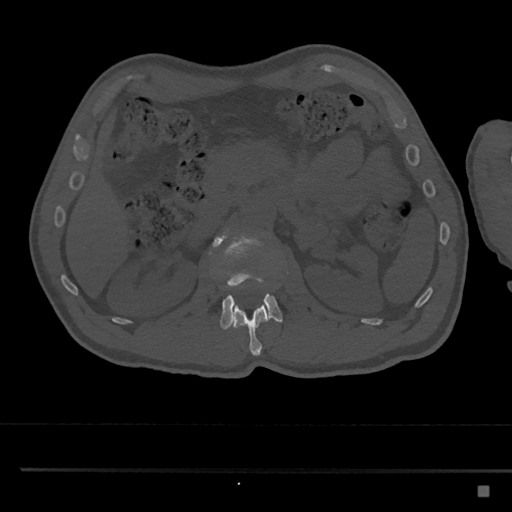
CT including the spine, one axial slice. Position 794 of 797 along the scan axis. 120 kVp. Bone window (W 1800 / L 400 HU). 0.5 mm slice thickness. 512 × 512 image matrix, field of view 391 × 391 mm. Male patient, age 59 years. From the clinical record (not read from this slice): primary cancer: prostate.
Outlined on this slice (semi-automatically segmented with operator editing):
- L1 vertebra: bounding box (x1, y1, x2, y2) in pixels: (233, 301, 270, 356)
- L2 vertebra: (209, 228, 283, 330)